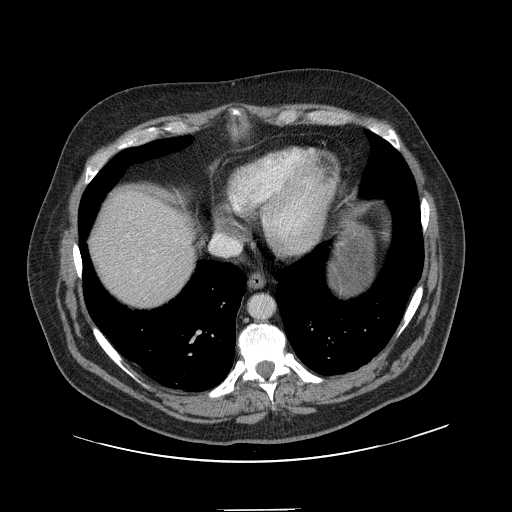
Contrast-enhanced abdominal CT, one axial slice; slice 135 of 154 in the series (ordered by position); 120 kVp; intravenous contrast given; soft-tissue window (W 400 / L 40 HU); 2.5 mm slice thickness; 512 × 512 image matrix, field of view 451 × 451 mm. Male patient, age 61 years. From the clinical record (not read from this slice): diagnosis: colorectal cancer liver metastases, imaged before liver resection.
Annotated regions visible in this slice (outlined manually by an expert reader):
- liver: box from (x=93, y=191) to (x=194, y=309) px
- planned liver remnant (the part of the liver to remain after resection): (x=93, y=191)–(x=195, y=308)